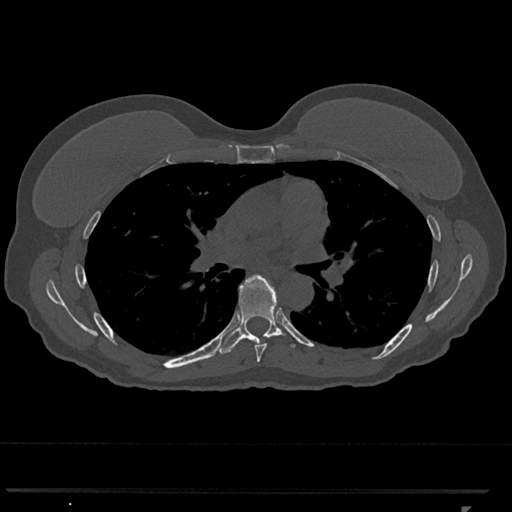
CT including the spine, one axial slice. Position 733 of 793 along the scan axis. Reconstruction kernel Br40s/3. 120 kVp. Bone window (W 1800 / L 400 HU). 0.5 mm slice thickness. 512 × 512 image matrix, field of view 380 × 380 mm. Patient: female, 62 years. Case-level facts recorded for this patient, not image findings: primary cancer: renal.
Outlined on this slice (semi-automatic segmentation, software-assisted and operator-edited):
- T6 vertebra: bounding box (x1, y1, x2, y2) in pixels: (254, 341, 267, 362)
- T7 vertebra: (217, 275, 296, 354)